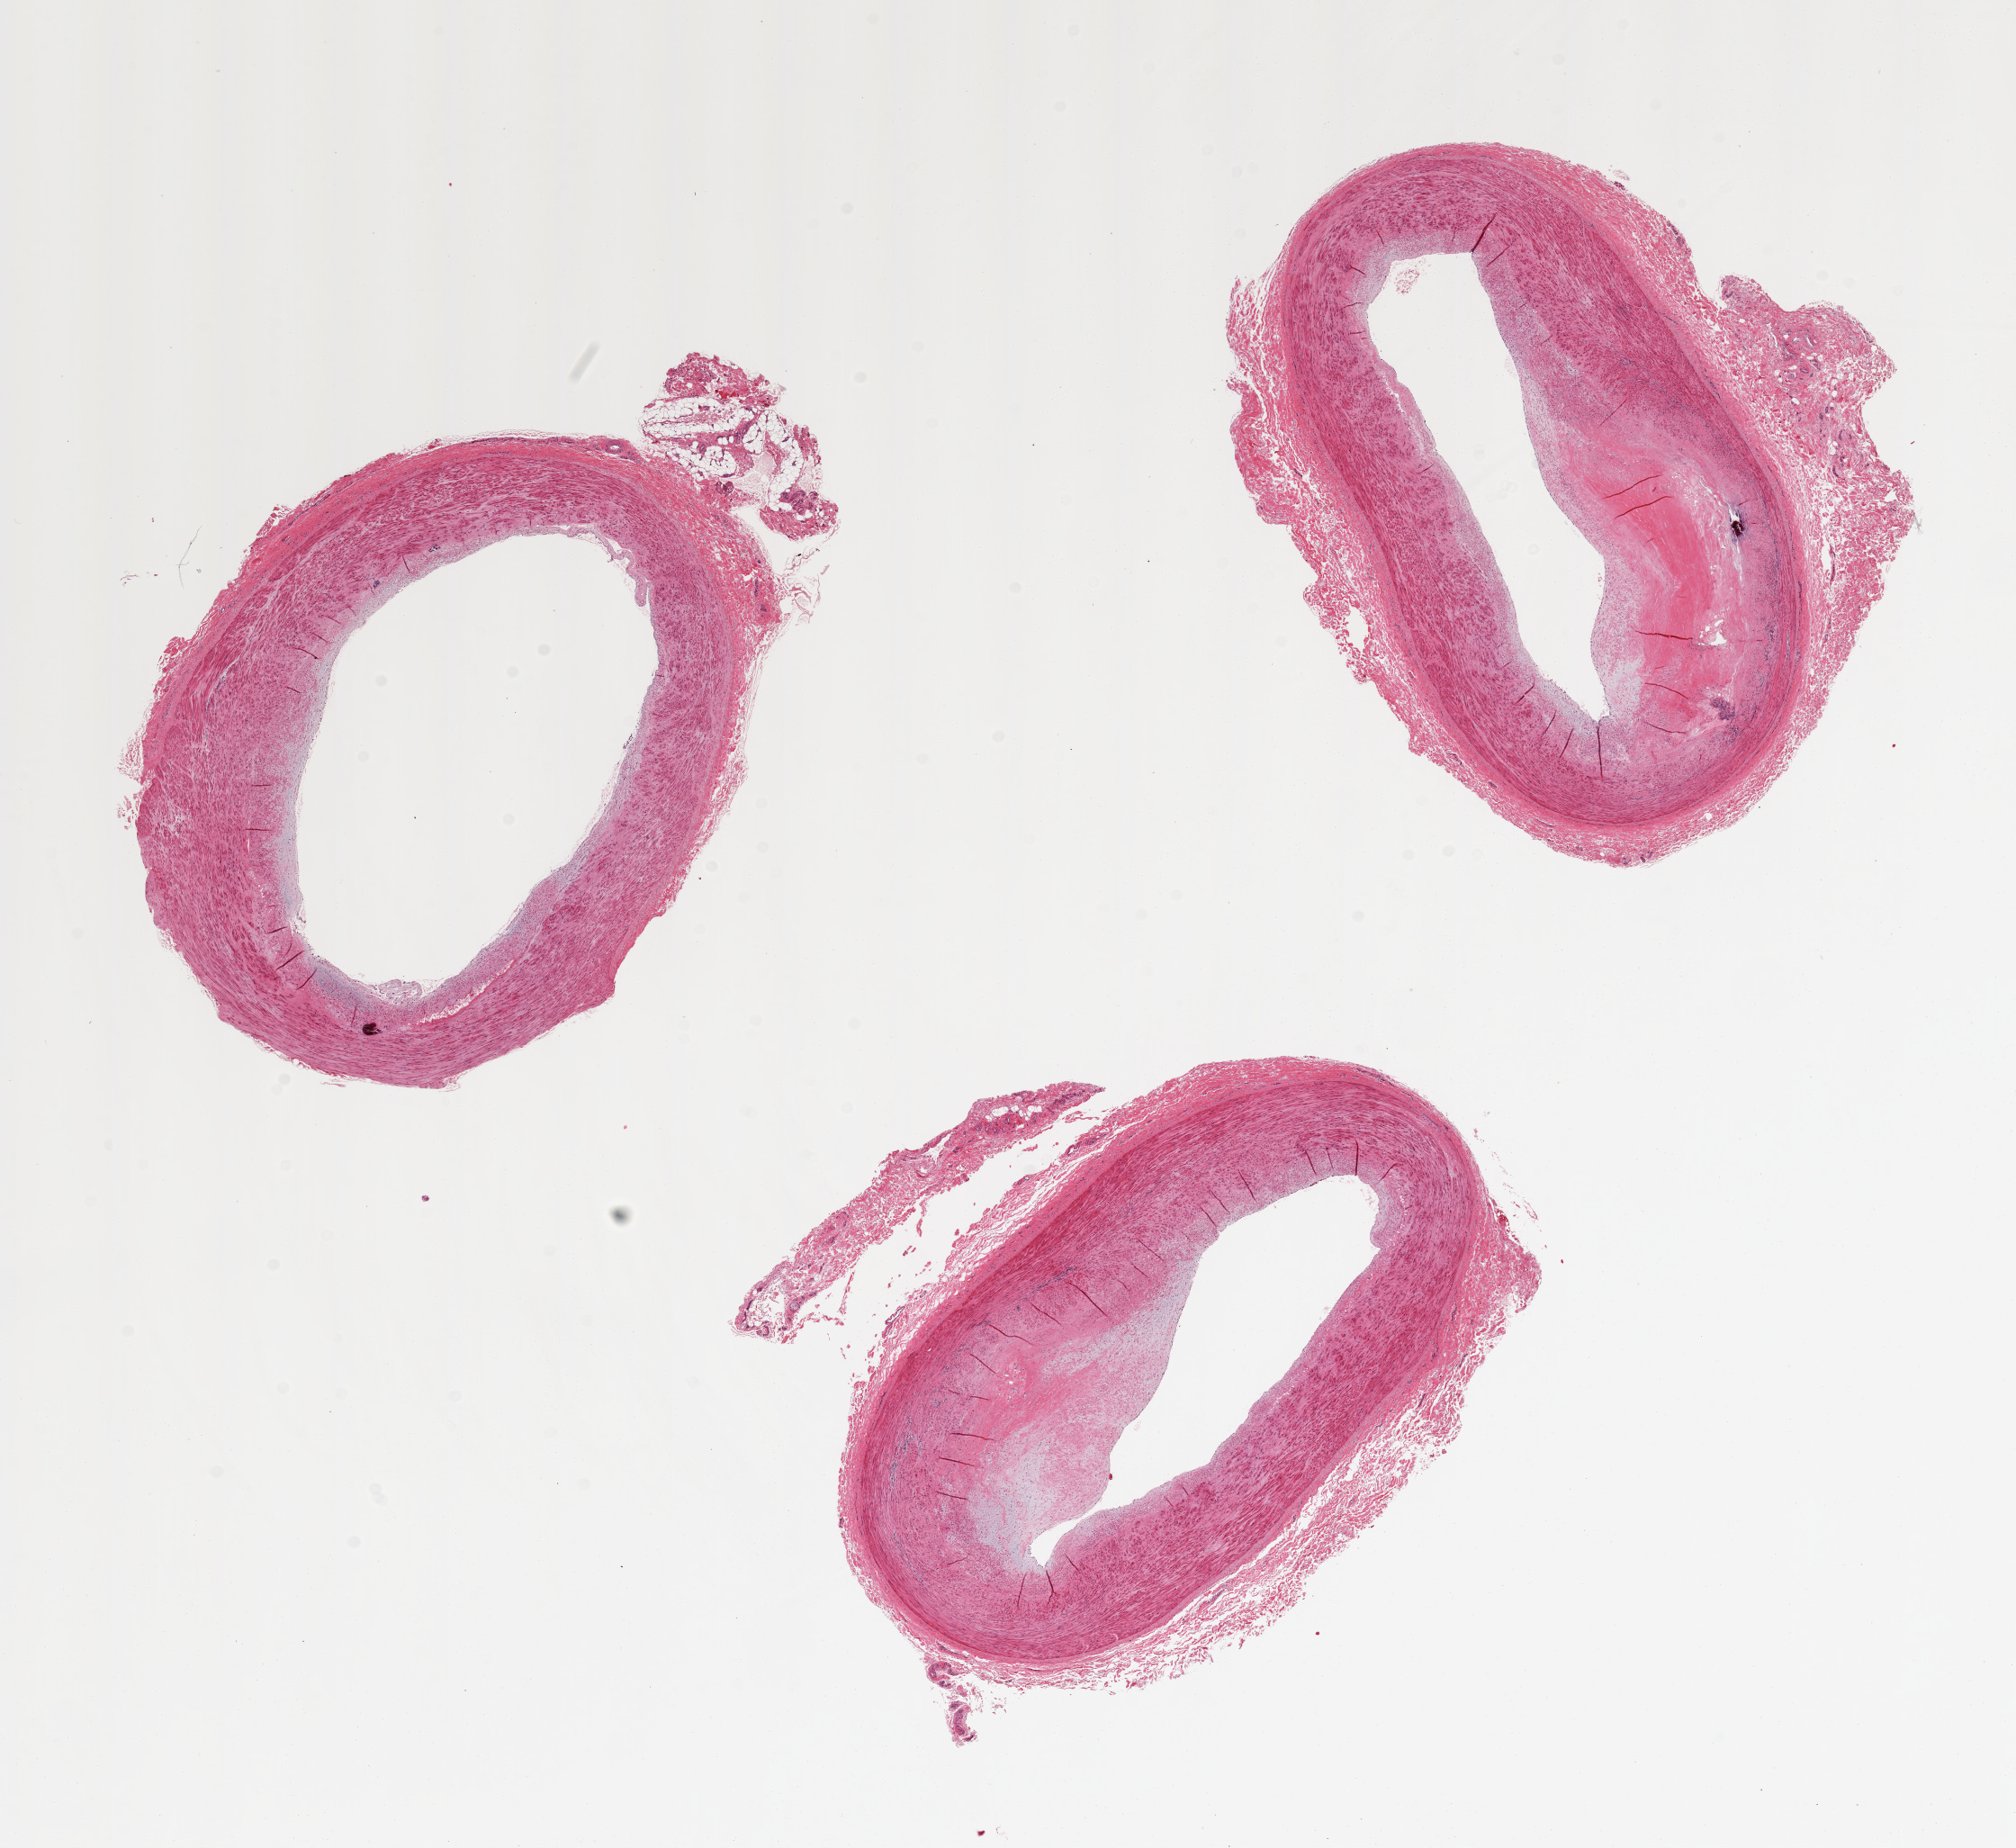
Whole-slide image, H&E stain — shown as a low-resolution overview of the whole scanned area (about 17.7 x 16.2 mm), PAXgene-fixed, paraffin-embedded tissue, section of tibial artery (target tissue), donor tissue sample. Male donor.
Review note (as recorded): 3 pieces; up to 30% occlusive atherosclerosis with focal calcification.